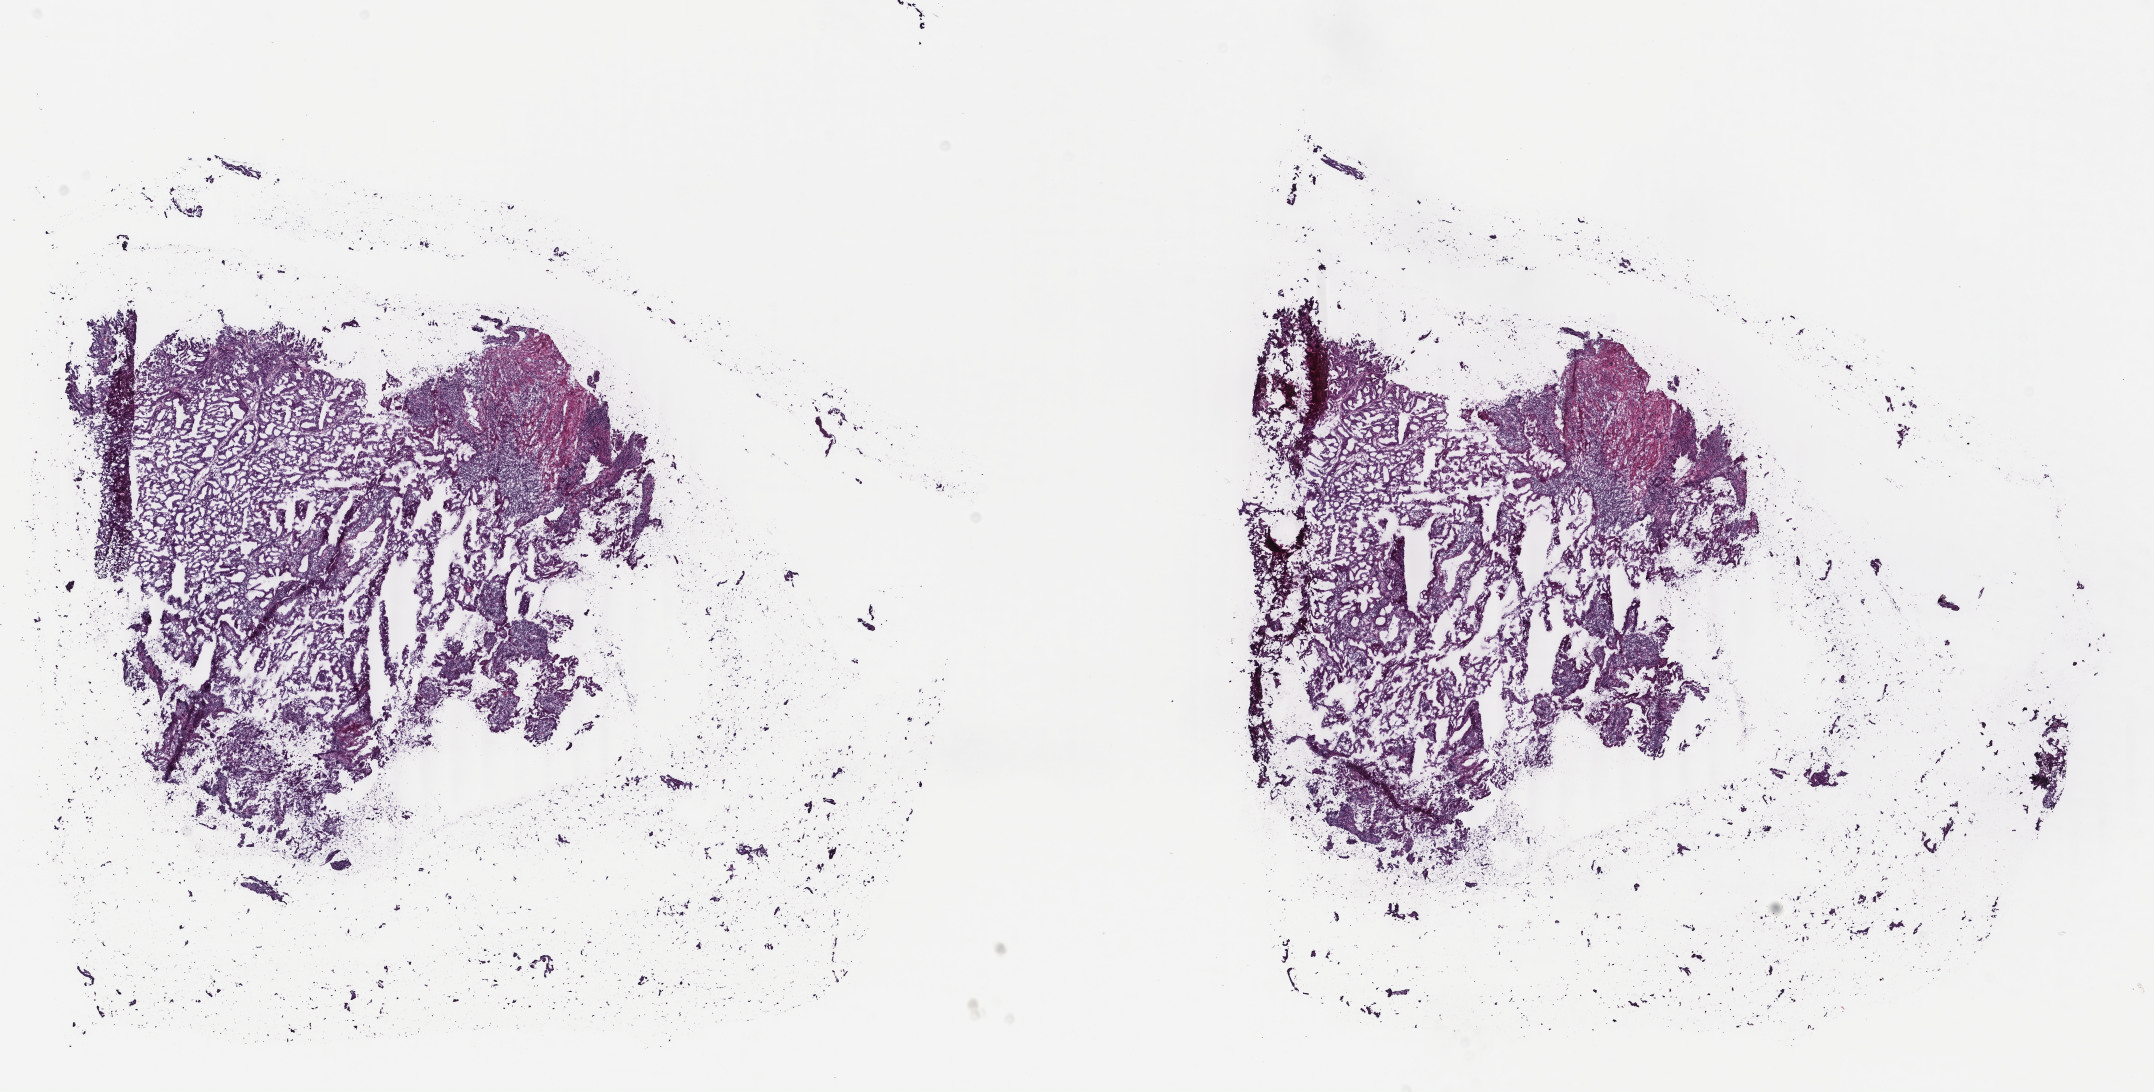
Digitized Hematoxylin and eosin (H&E) stained tissue section (whole slide), shown as a low-resolution overview of the whole scanned area (about 17.1 x 8.7 mm, from a 40x scan), frozen section from the top of the tissue portion, sample: primary tumour, uterus. Patient: female, age at initial diagnosis 69 years. Histologic grade: G1 (well differentiated). Pathologist review of this section (percent, as recorded): tumour cells 65%, tumour nuclei 70%, normal cells 0%, stromal cells 30%, necrosis 5%. Infiltration values recorded for this section: lymphocyte infiltration 35%, monocyte infiltration 0%, neutrophil infiltration 0%.
FIGO stage: IA. Pathologic diagnosis: Endometrioid adenocarcinoma, NOS (endometrium).